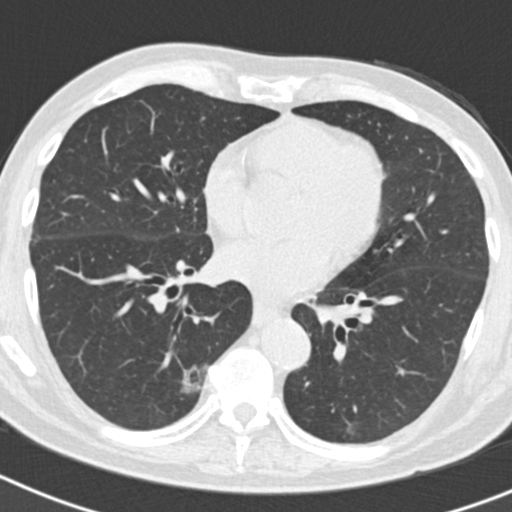
Low-dose screening chest CT, axial slice; second annual screen; lung window (W 1500 / L -600 HU); 2 mm slice thickness; slice 96 of 186 in the series; 512 × 512 image matrix. Male, age 70 years at enrolment.
Expert-annotated lung lesion, bounding box [x1, y1, x2, y2] px = [125, 358, 209, 430]. The screening reader recorded 5 non-calcified nodules or masses ≥4 mm on this exam (right lower lobe, right lower lobe, right upper lobe, right upper lobe, left upper lobe); which of them this box marks is not recorded. Official screen result: positive, other. Later outcome: lung cancer diagnosed 622 days after this screen — bronchiolo-alveolar adenocarcinoma, NOS, right lower lobe, poorly differentiated (G3), stage IB (AJCC 6th edition), 30 mm at pathology.